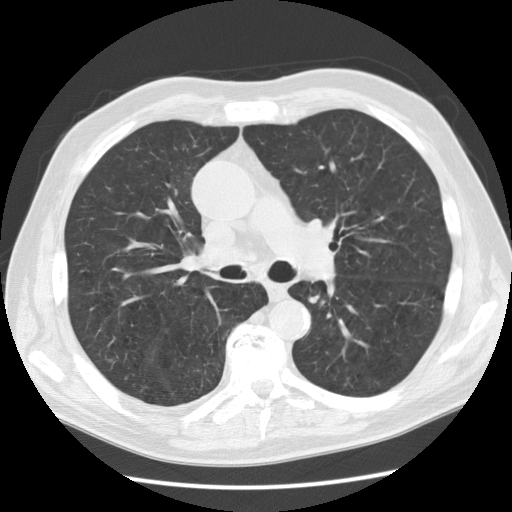
Axial slice from a low-dose chest CT screening exam. Second annual screen. Lung window (W 1500 / L -600 HU). Slice 52 of 130 in the series. 512 × 512 image matrix. Male participant, aged 73 years at enrolment. Current smoker at enrolment.
- Expert reader's lesion annotation, bounding box (x1, y1, x2, y2) in pixels: (294, 277, 338, 317).
- The screening reader recorded 4 non-calcified nodules or masses ≥4 mm on this exam (right upper lobe, right upper lobe, left upper lobe, right lower lobe); which of them this box marks is not recorded.
- Later outcome: lung cancer diagnosed 302 days after this screen — small cell carcinoma, NOS, left lower lobe, stage IIIB (AJCC 6th edition), 55 mm at pathology.